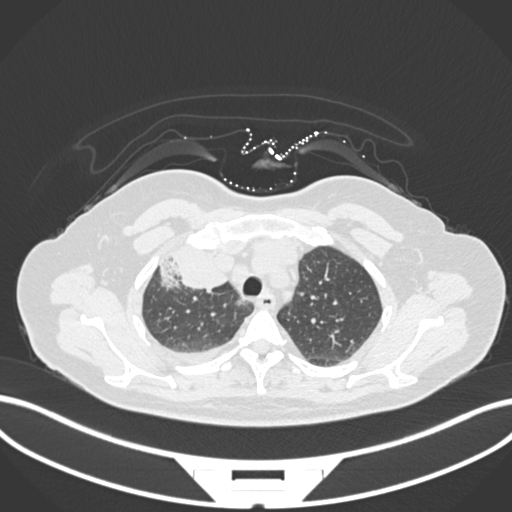
Chest CT, one axial slice; position 131 of 172 along the scan axis; lung window (W 1500 / L -600 HU); 1 mm slice thickness; 512 × 512 image matrix, field of view 400 × 400 mm. Female patient, age 52 years. Case-level facts recorded for this patient, not image findings: clinical TNM (as recorded): T3 N1 M1.
Structures marked on this image (rectangle marked by the reading radiologist):
- lung tumour (recorded histology: adenocarcinoma): bounding box (x1, y1, x2, y2) in pixels: (158, 242, 232, 292)